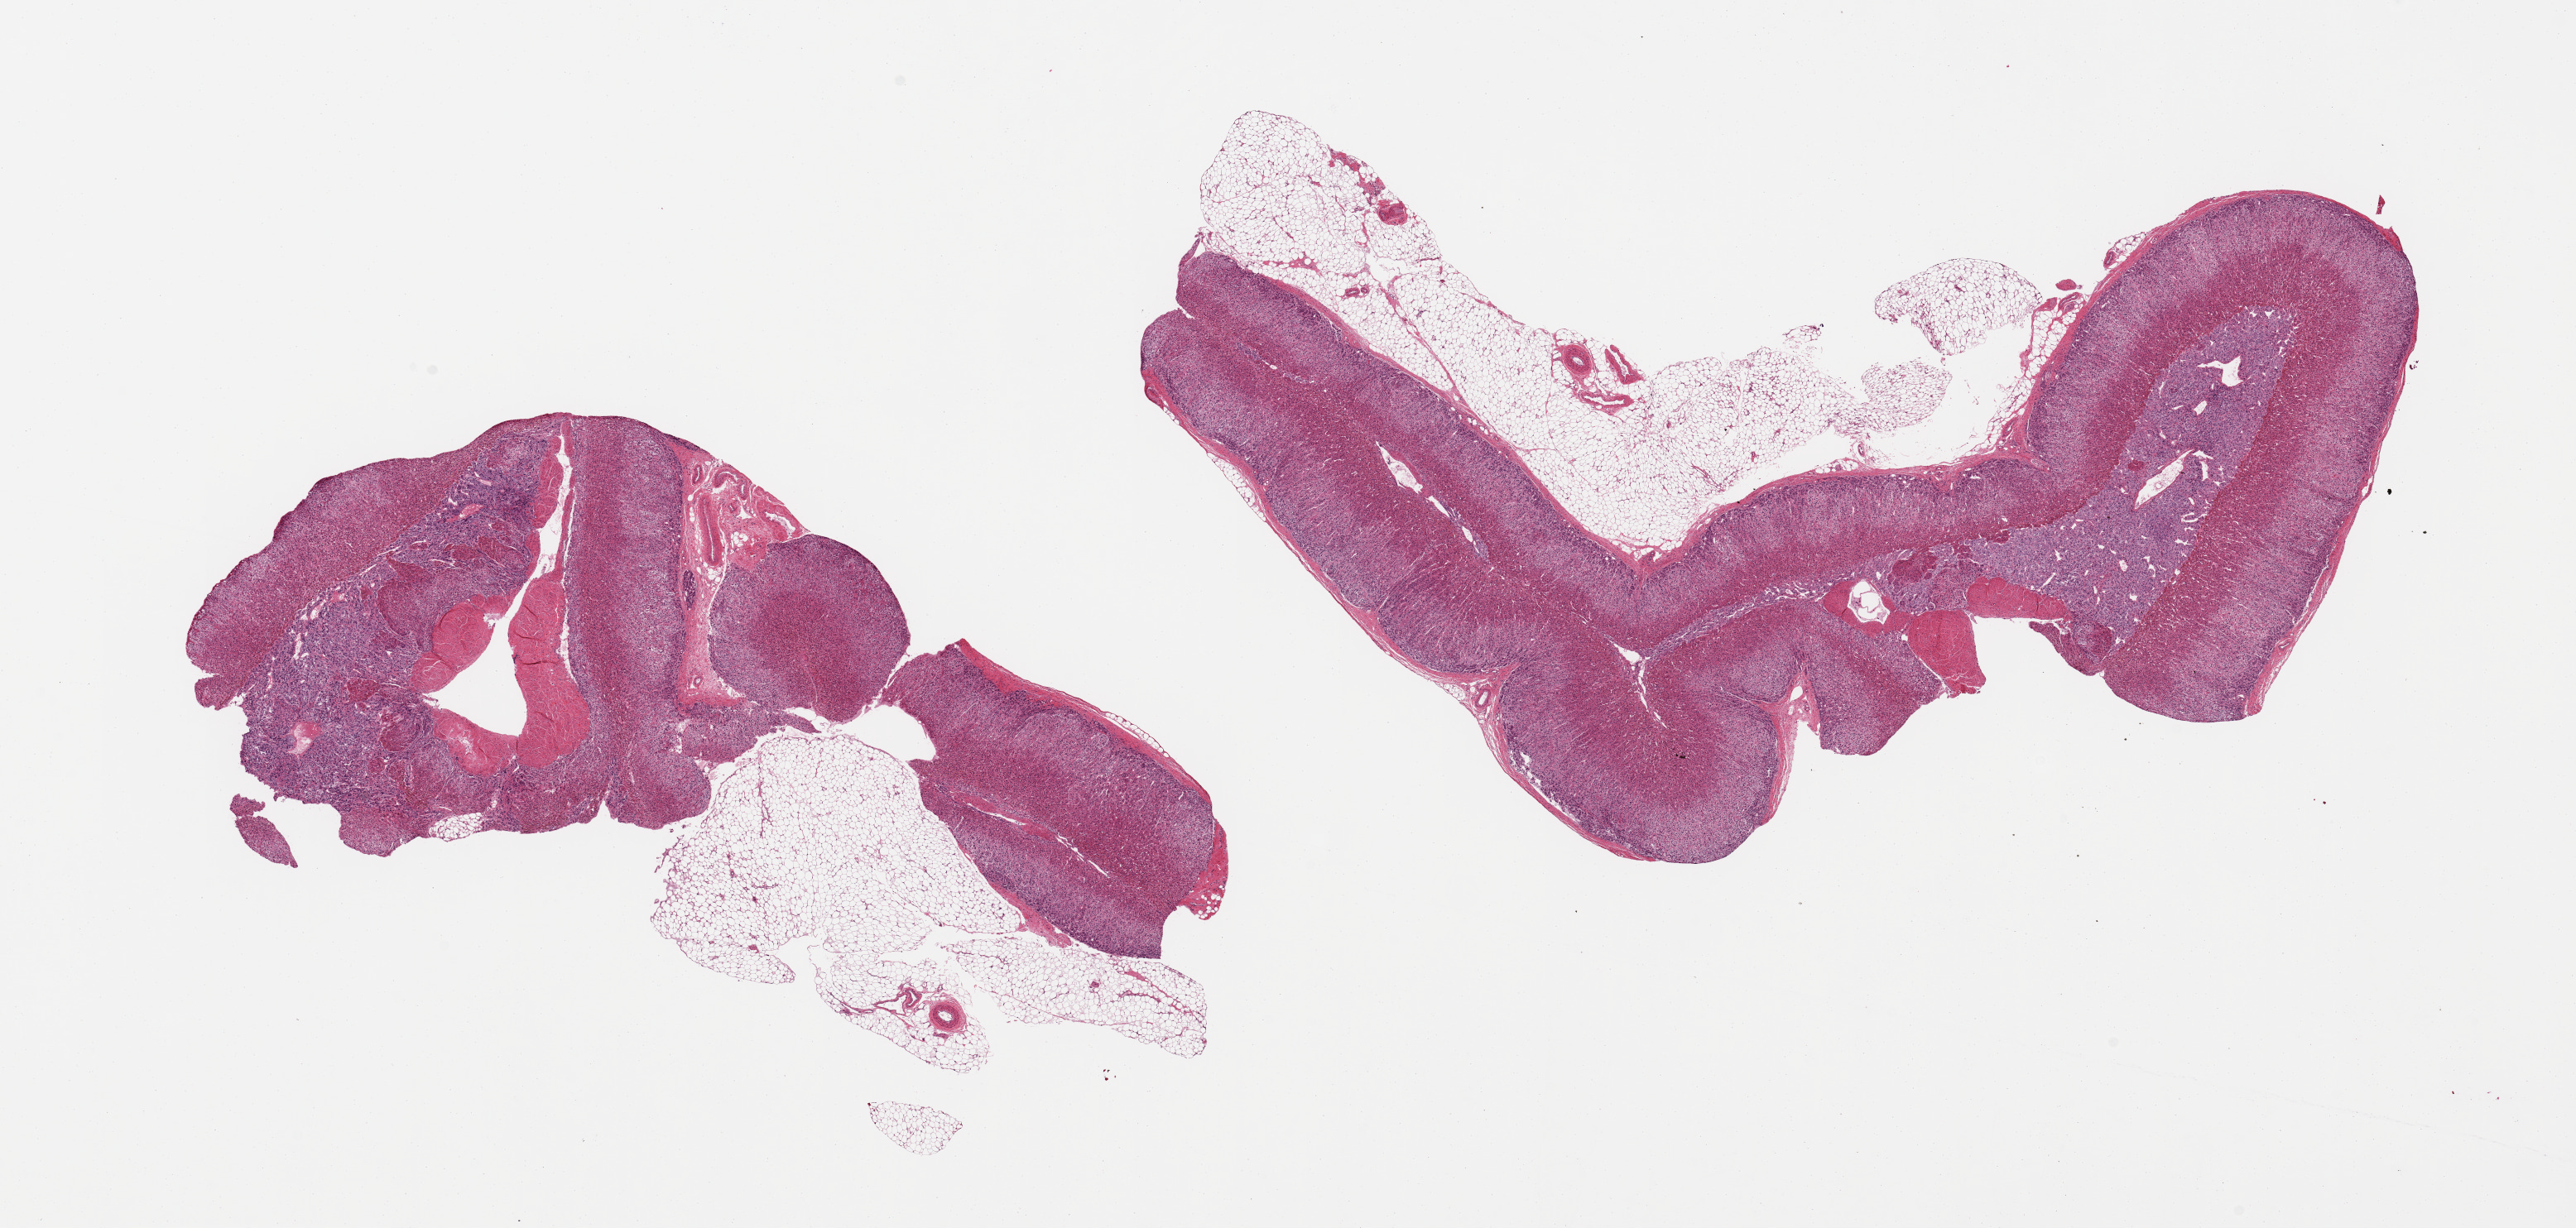
Whole-slide image, H&E stain — low-resolution overview of the scanned area, about 24.6 x 11.7 mm (slide scanned at 20x). PAXgene-fixed, paraffin-embedded tissue. Section of adrenal gland (target tissue). Tissue donor sample. Donor sex: male.
- reviewer comment on this tissue sample: 2 pieces, well preserved; prominent medulla in one section, ~3.5x1.5mmm valuable specimen; Adherent fat up to ~1-2mm